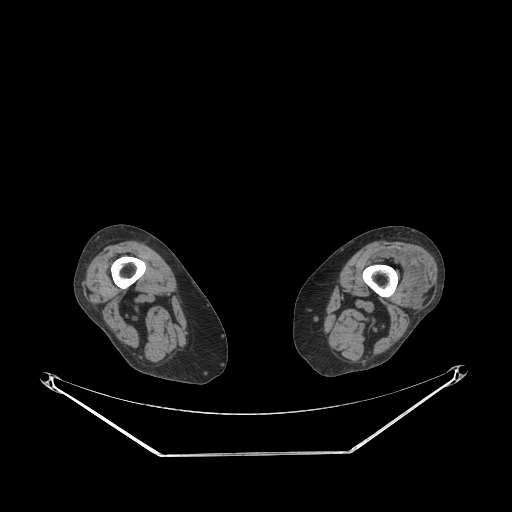
CT of an extremity soft-tissue mass (from a PET/CT study), one axial slice. Position 192 of 267 along the scan axis. Reconstruction kernel STANDARD. 140 kVp. Soft-tissue window (W 400 / L 40 HU). 3.75 mm slice thickness. 512 × 512 image matrix, field of view 500 × 500 mm. Female patient. Case-level facts recorded for this patient, not image findings: histological type: undifferentiated – high grade; grade: high; site of the primary tumour: left thigh.
Annotated regions visible in this slice (expert contour drawn on MRI and transferred to this co-registered scan by the dataset authors):
- gross tumour volume including surrounding oedema: box from (x=381, y=253) to (x=424, y=296) px